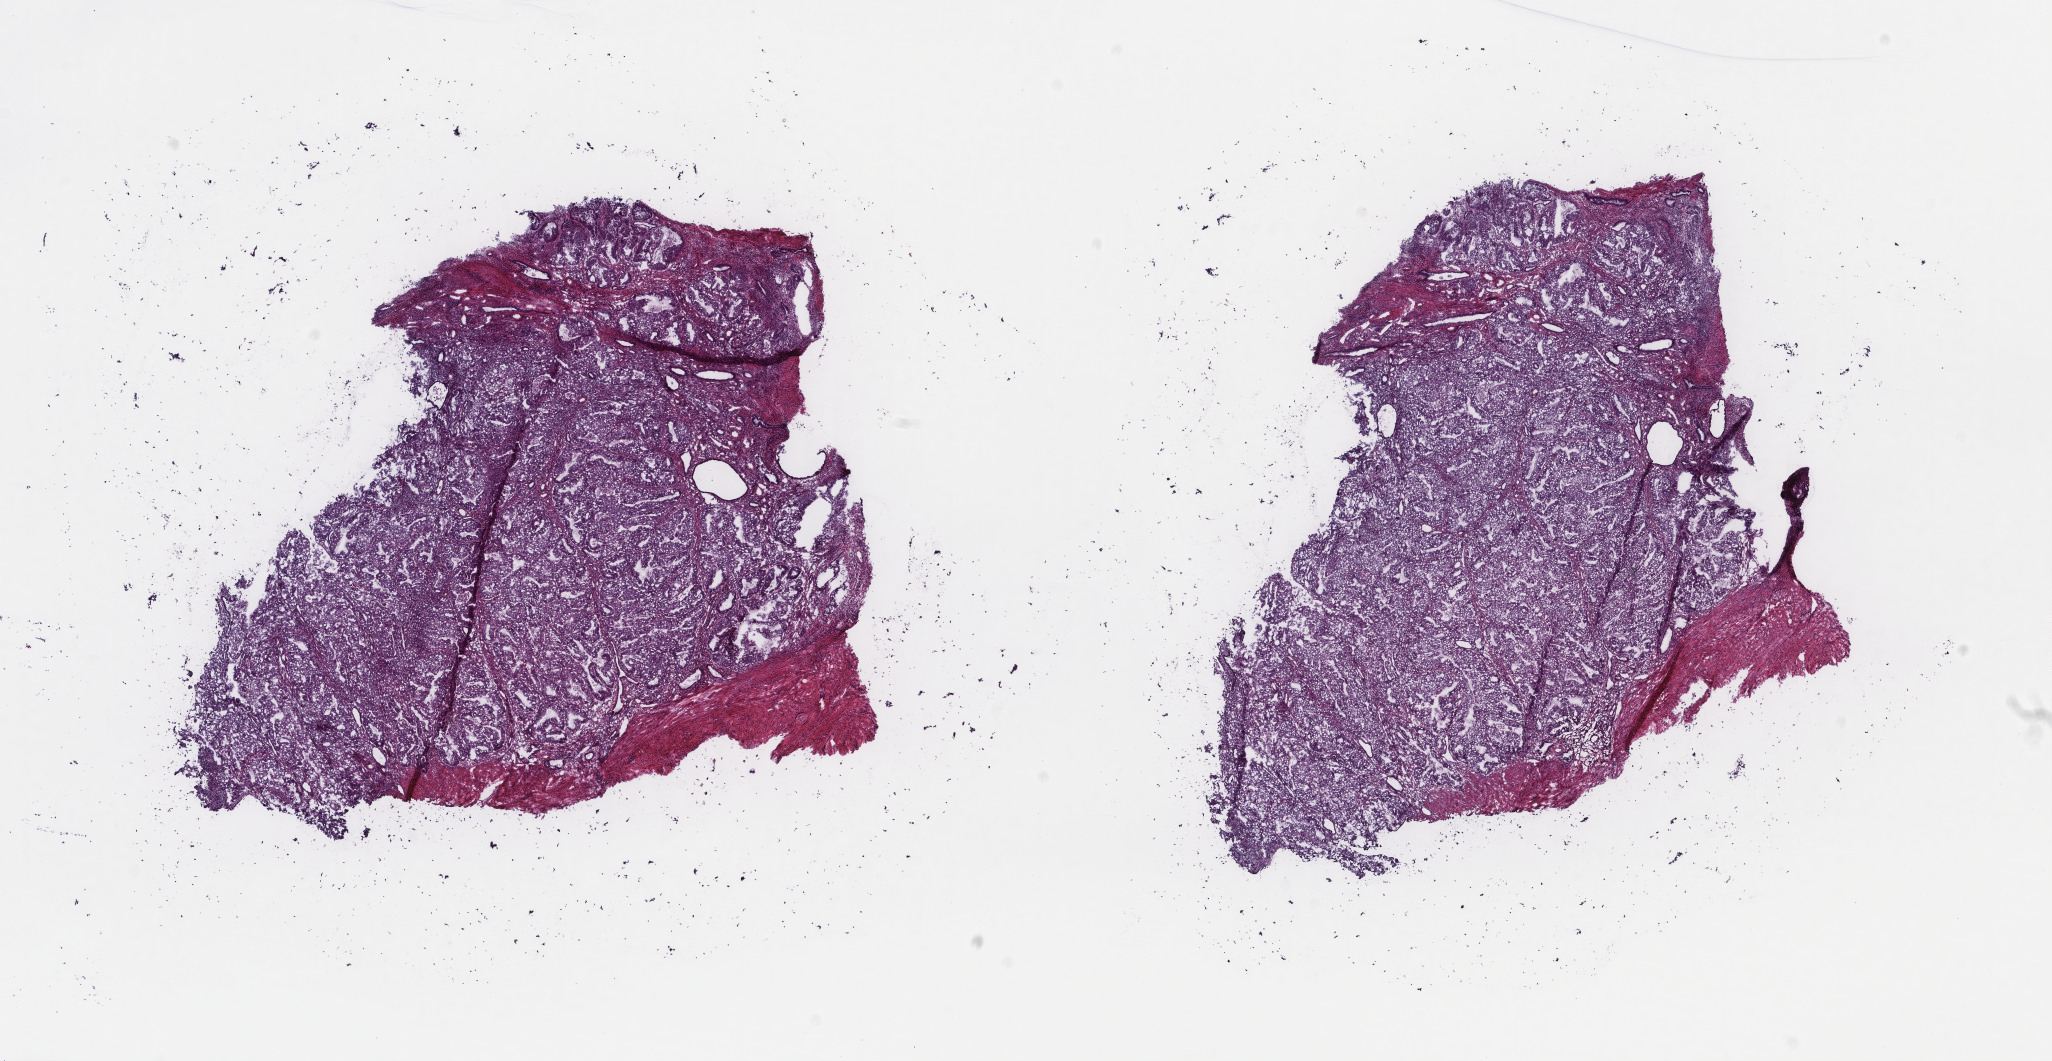
Digitized H&E tissue section (whole slide) — low-resolution overview of the scanned area, about 16.3 x 8.4 mm (acquisition: 40x scan), frozen section from the top of the tissue portion, uterus, primary tumour sample. Patient: female, age at initial diagnosis 46 years. Slide review estimates, as recorded: tumour cells 85%, tumour nuclei 80%.
Diagnosis: Endometrioid adenocarcinoma, NOS (endometrium).